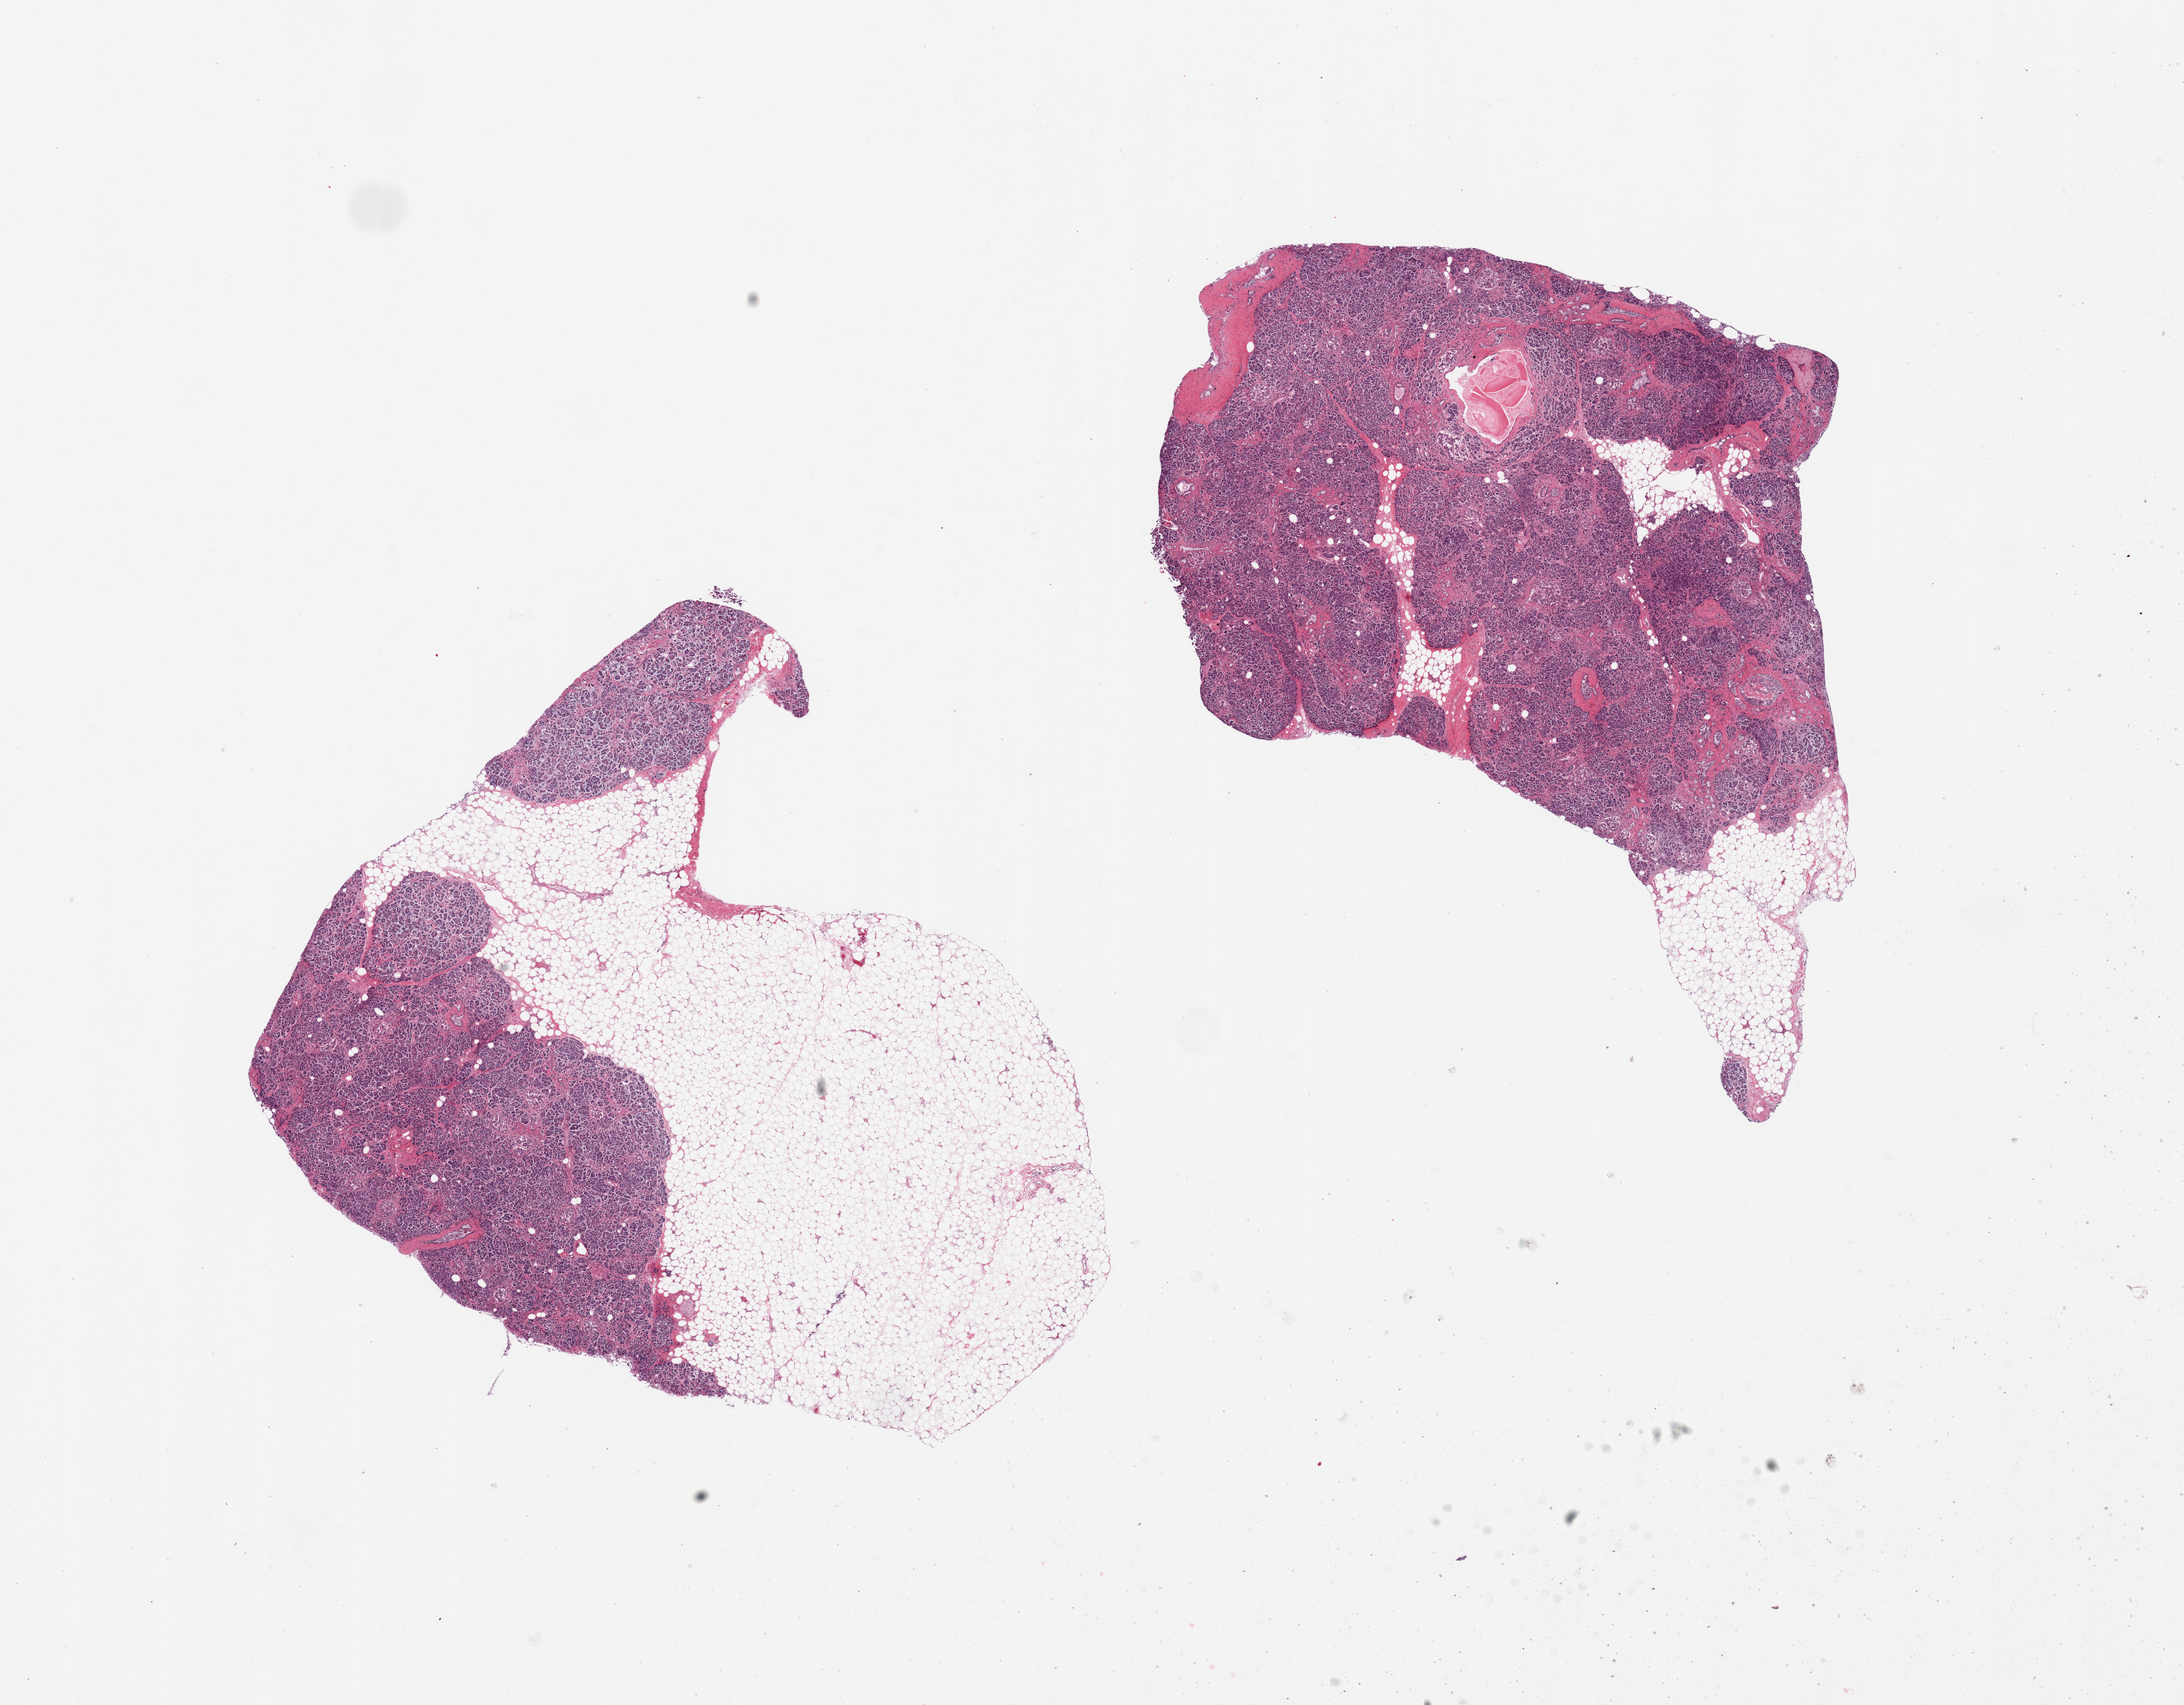
H&E whole-slide image, shown as a low-resolution overview of the whole scanned area (about 22.6 x 17.7 mm); PAXgene-fixed paraffin-embedded (PFPE) section; target tissue: pancreas; tissue donor sample.
Review note (as recorded): 2 pieces; one piece with 60% external fat, fibrosis, PanIN 1.